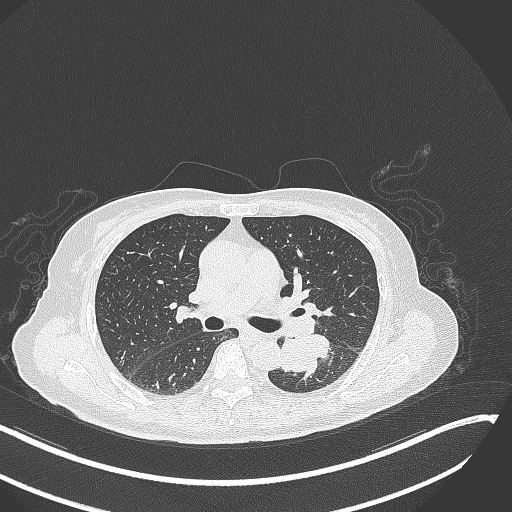
Chest CT, one axial slice. Slice 168 of 342 in the series (ordered by position). Reconstruction kernel B70f. 120 kVp. Lung window (W 1500 / L -600 HU). 512 × 512 image matrix, field of view 400 × 400 mm. Patient: female, 64 years. Case-level facts recorded for this patient, not image findings: clinical TNM (as recorded): T3 N1 M1.
Outlined on this slice (rectangle marked by the reading radiologist):
- lung tumour (recorded histology: small cell carcinoma): bounding box (x1, y1, x2, y2) in pixels: (278, 334, 334, 378)